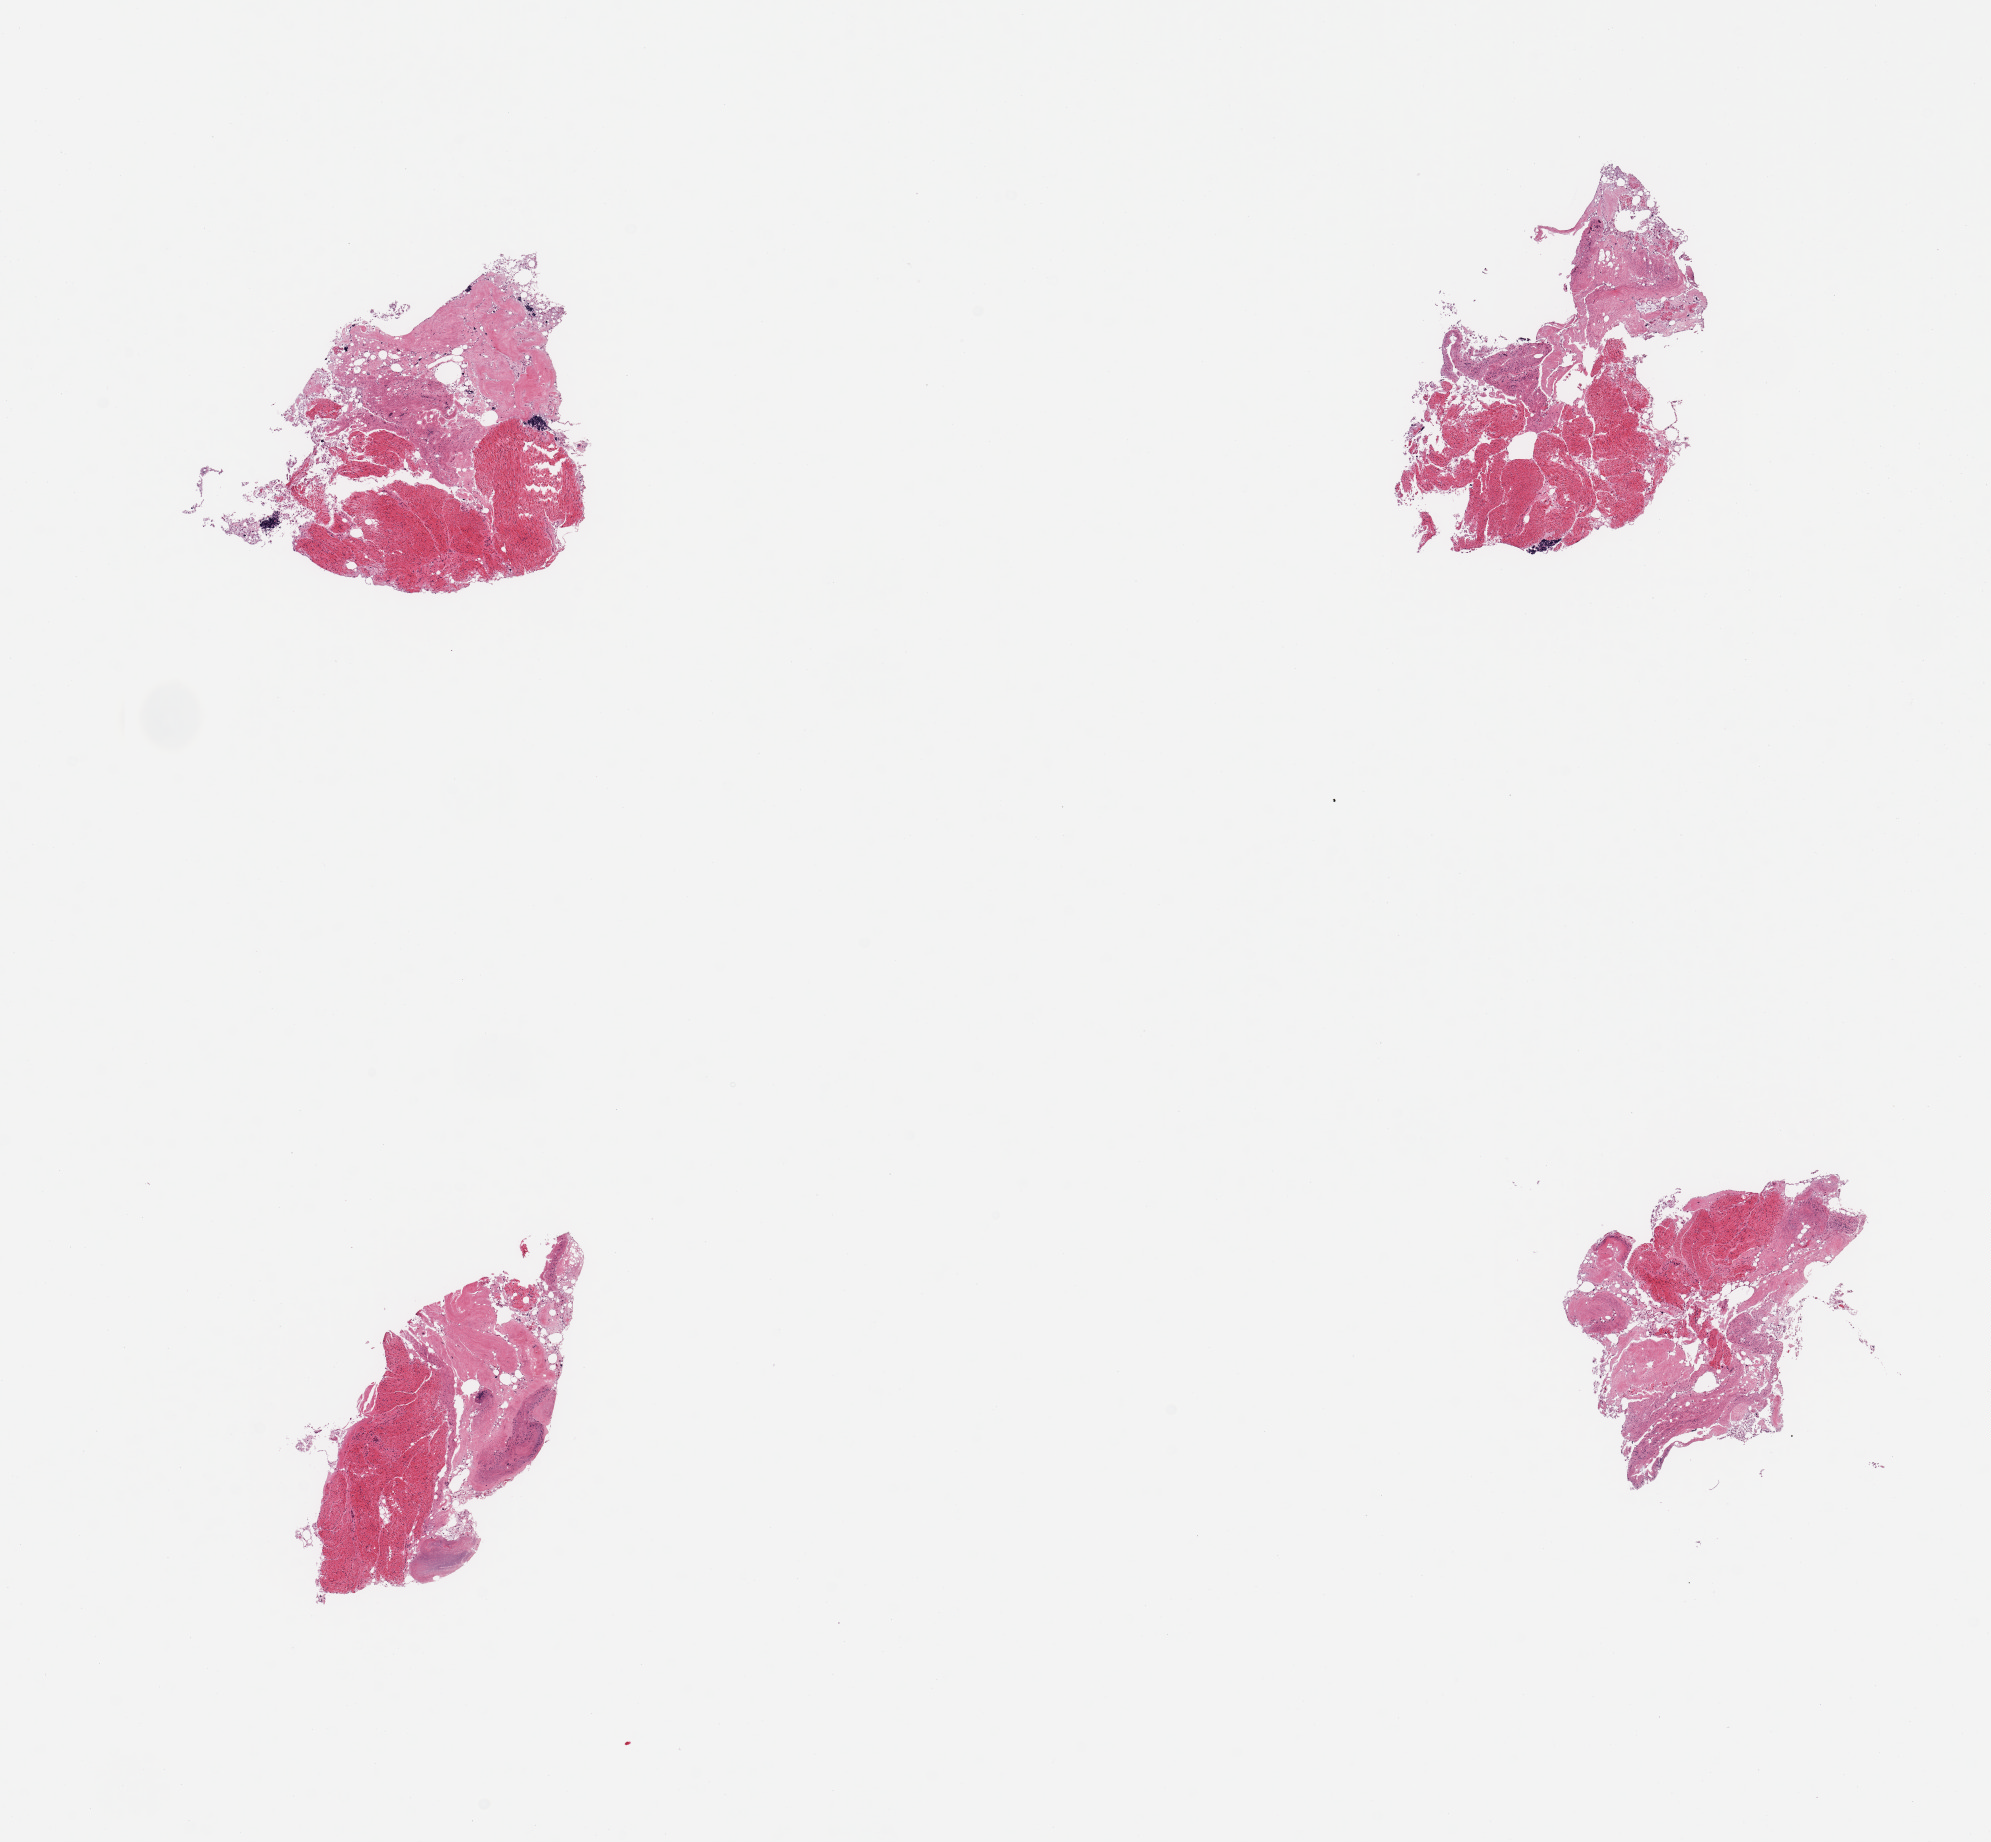
Whole-slide image, hematoxylin and eosin (H&E) stain — low-resolution overview of the scanned area, about 15.8 x 14.6 mm. PAXgene-fixed, paraffin-embedded tissue. Target tissue: ileum. Donor tissue sample. Donor sex: female.
Reviewer comment on this tissue sample: 4 pieces; insufficient lymphoid tissue; mucosa autolyzed.